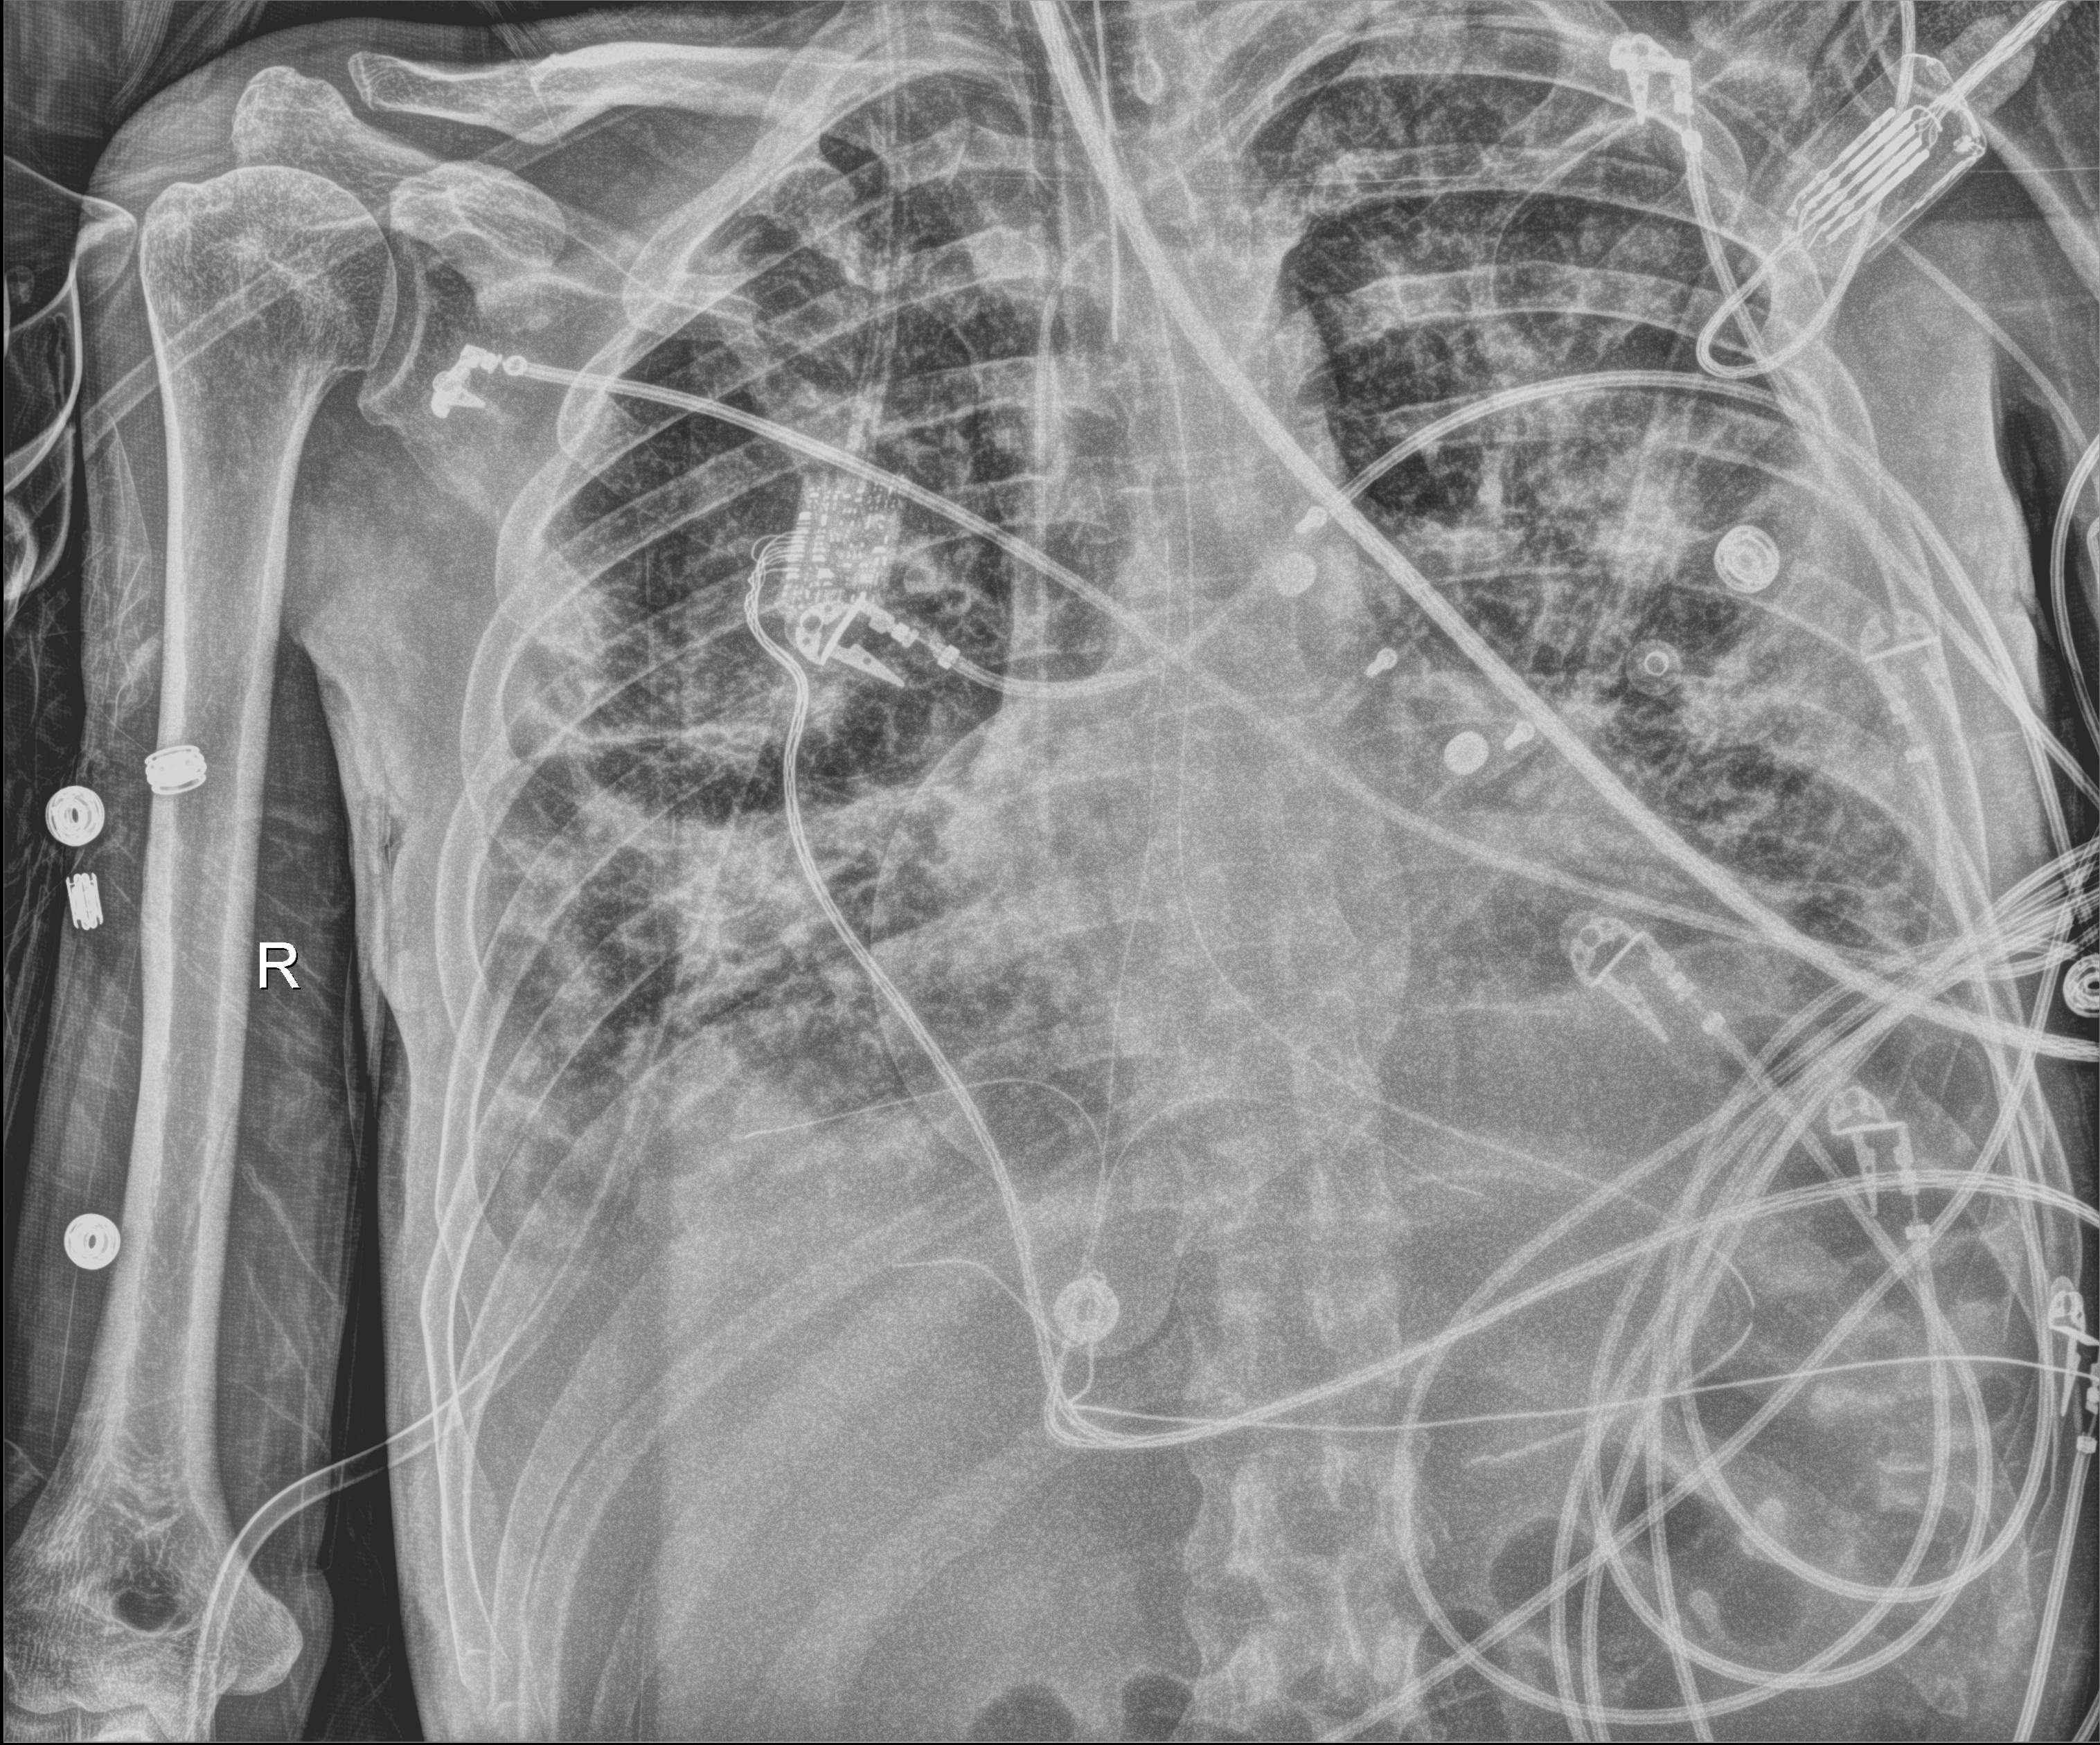
Portable chest radiograph. Patient hospitalised with COVID-19; male, aged 18–59 years.
From the hospital-stay record, not from the radiograph (when in the stay this image was taken is not recorded):
- other chronic lung disease (admission record): no